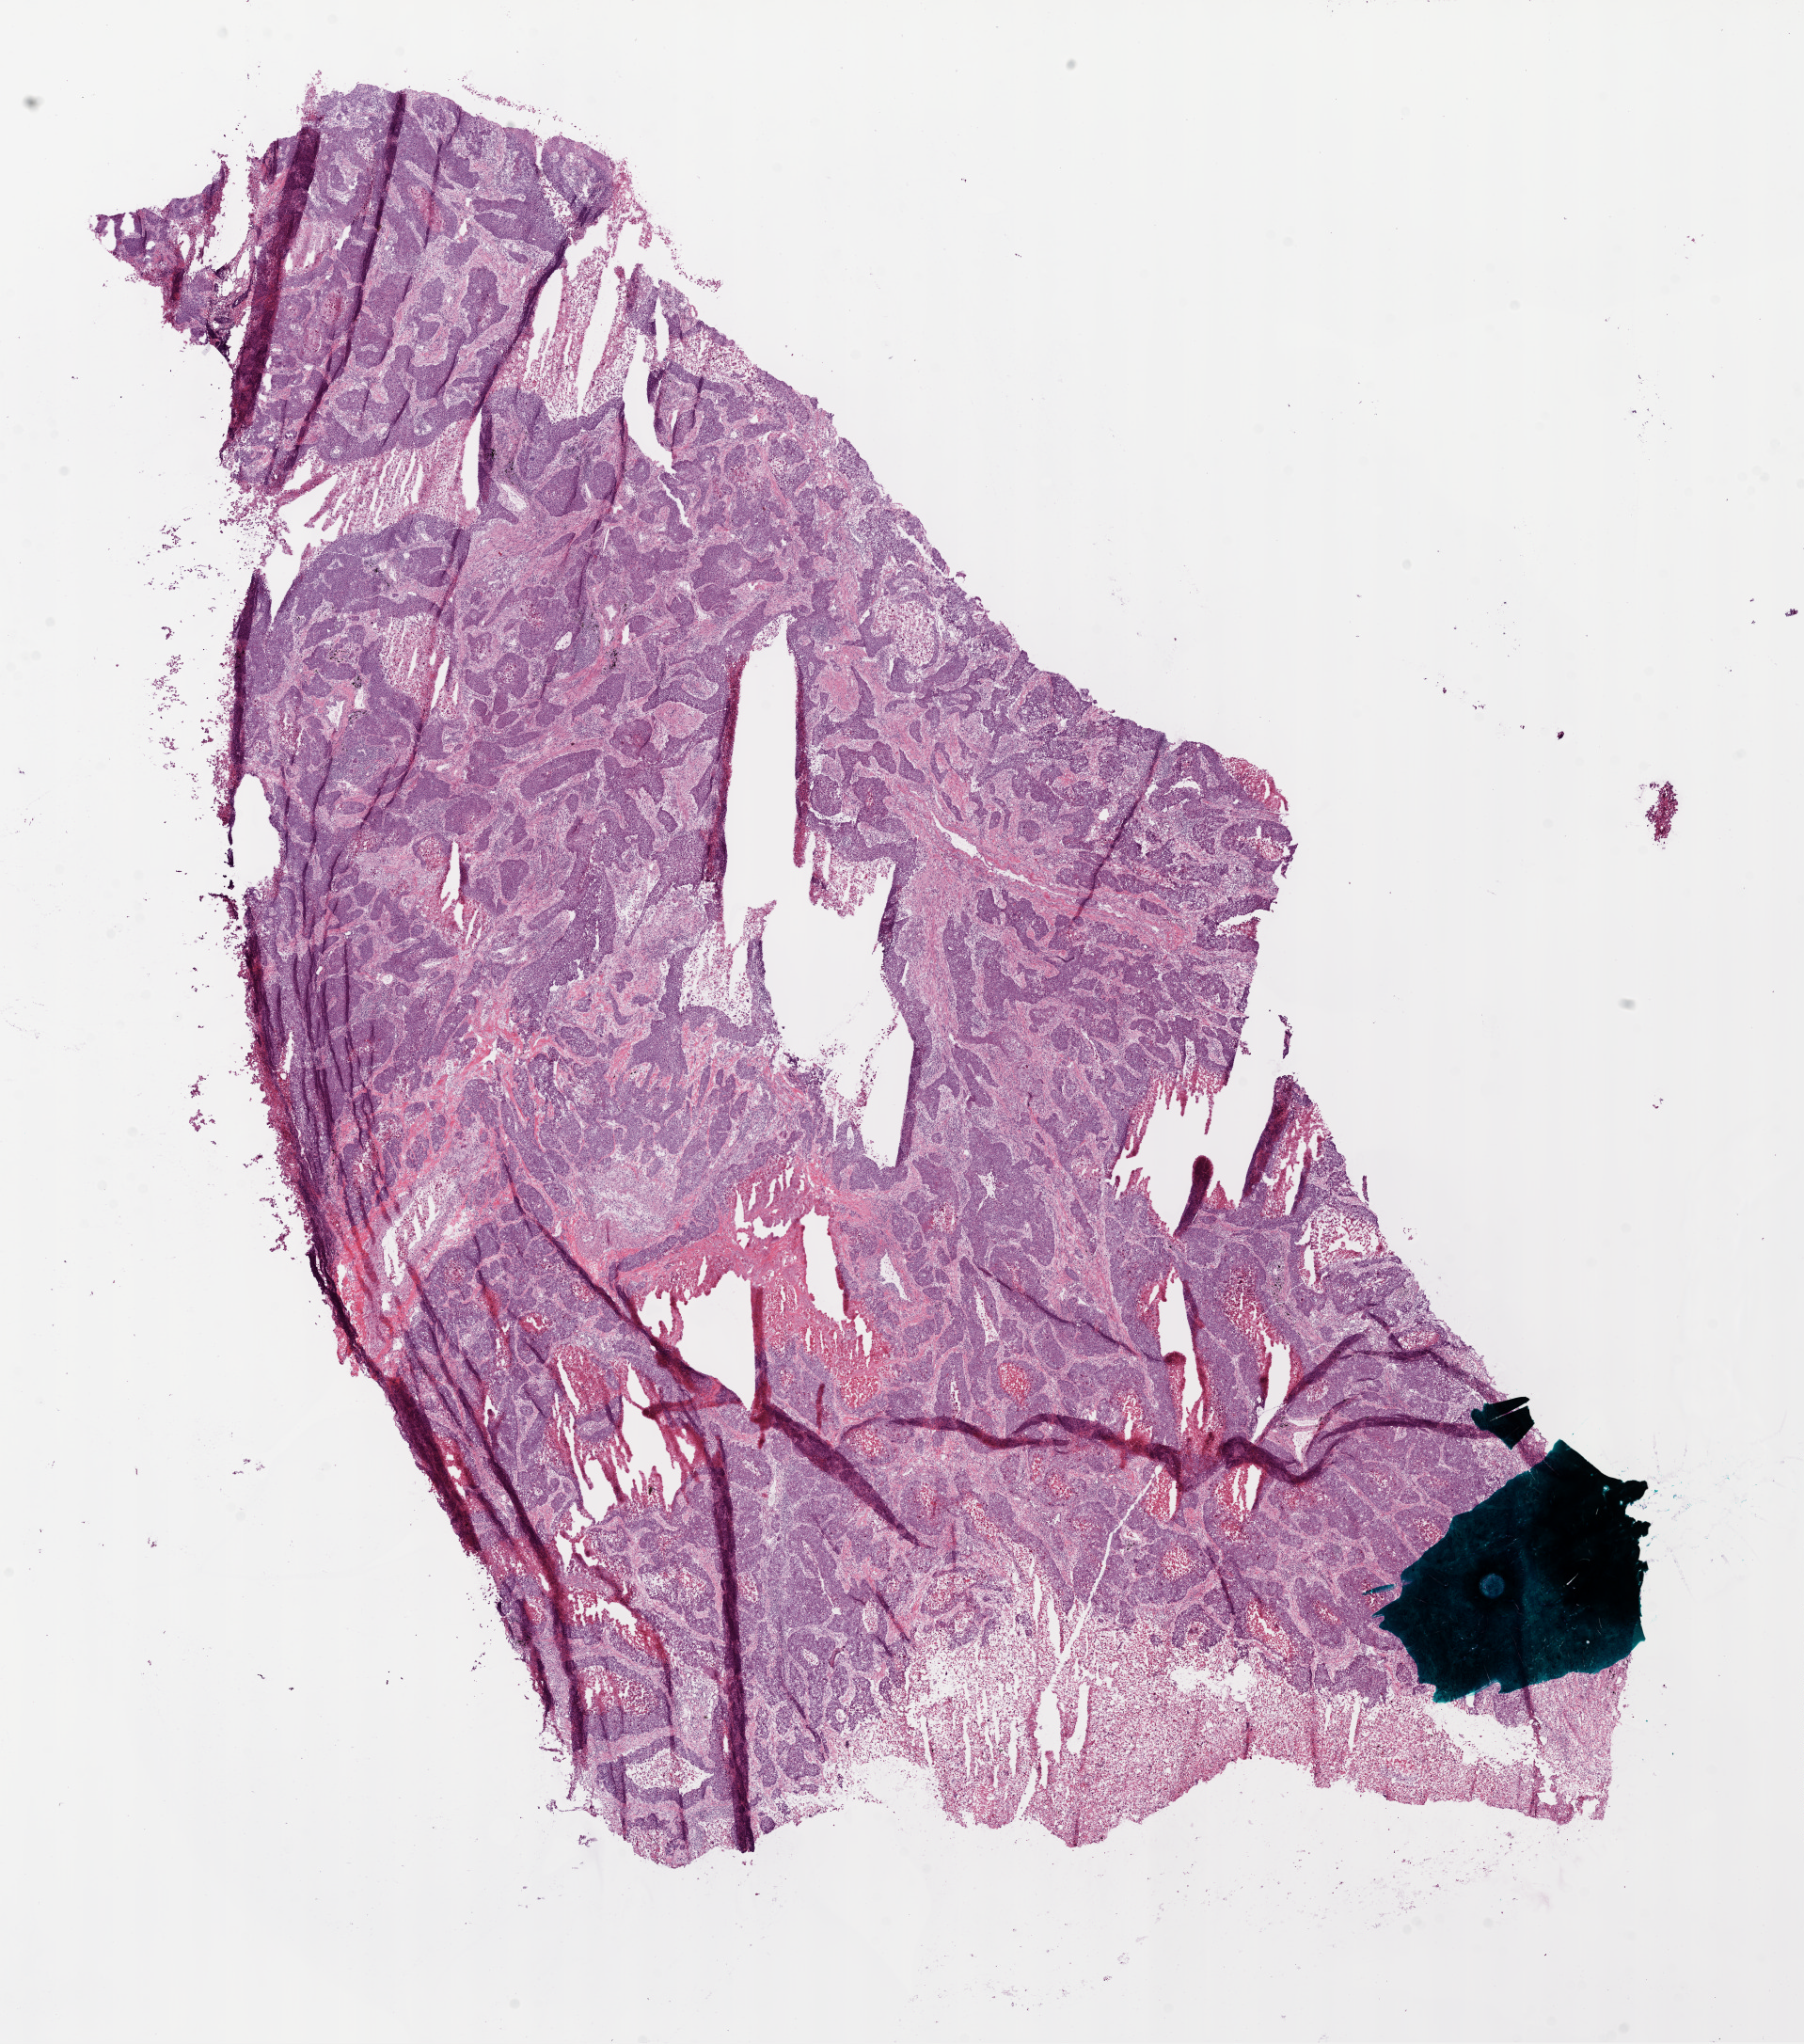
Digitized H&E tissue section (whole slide), low-resolution overview of the scanned area, about 15.5 x 17.5 mm (acquisition: 20x scan); frozen section from the bottom of the tissue portion; primary tumour sample from the lung. Male, age 66 years at initial diagnosis. Pathologist review of this section (percent, as recorded): tumour nuclei 90%, necrosis 10%.
* pathologic diagnosis: Squamous cell carcinoma, NOS
* laterality: left
* AJCC pathologic stage: IB